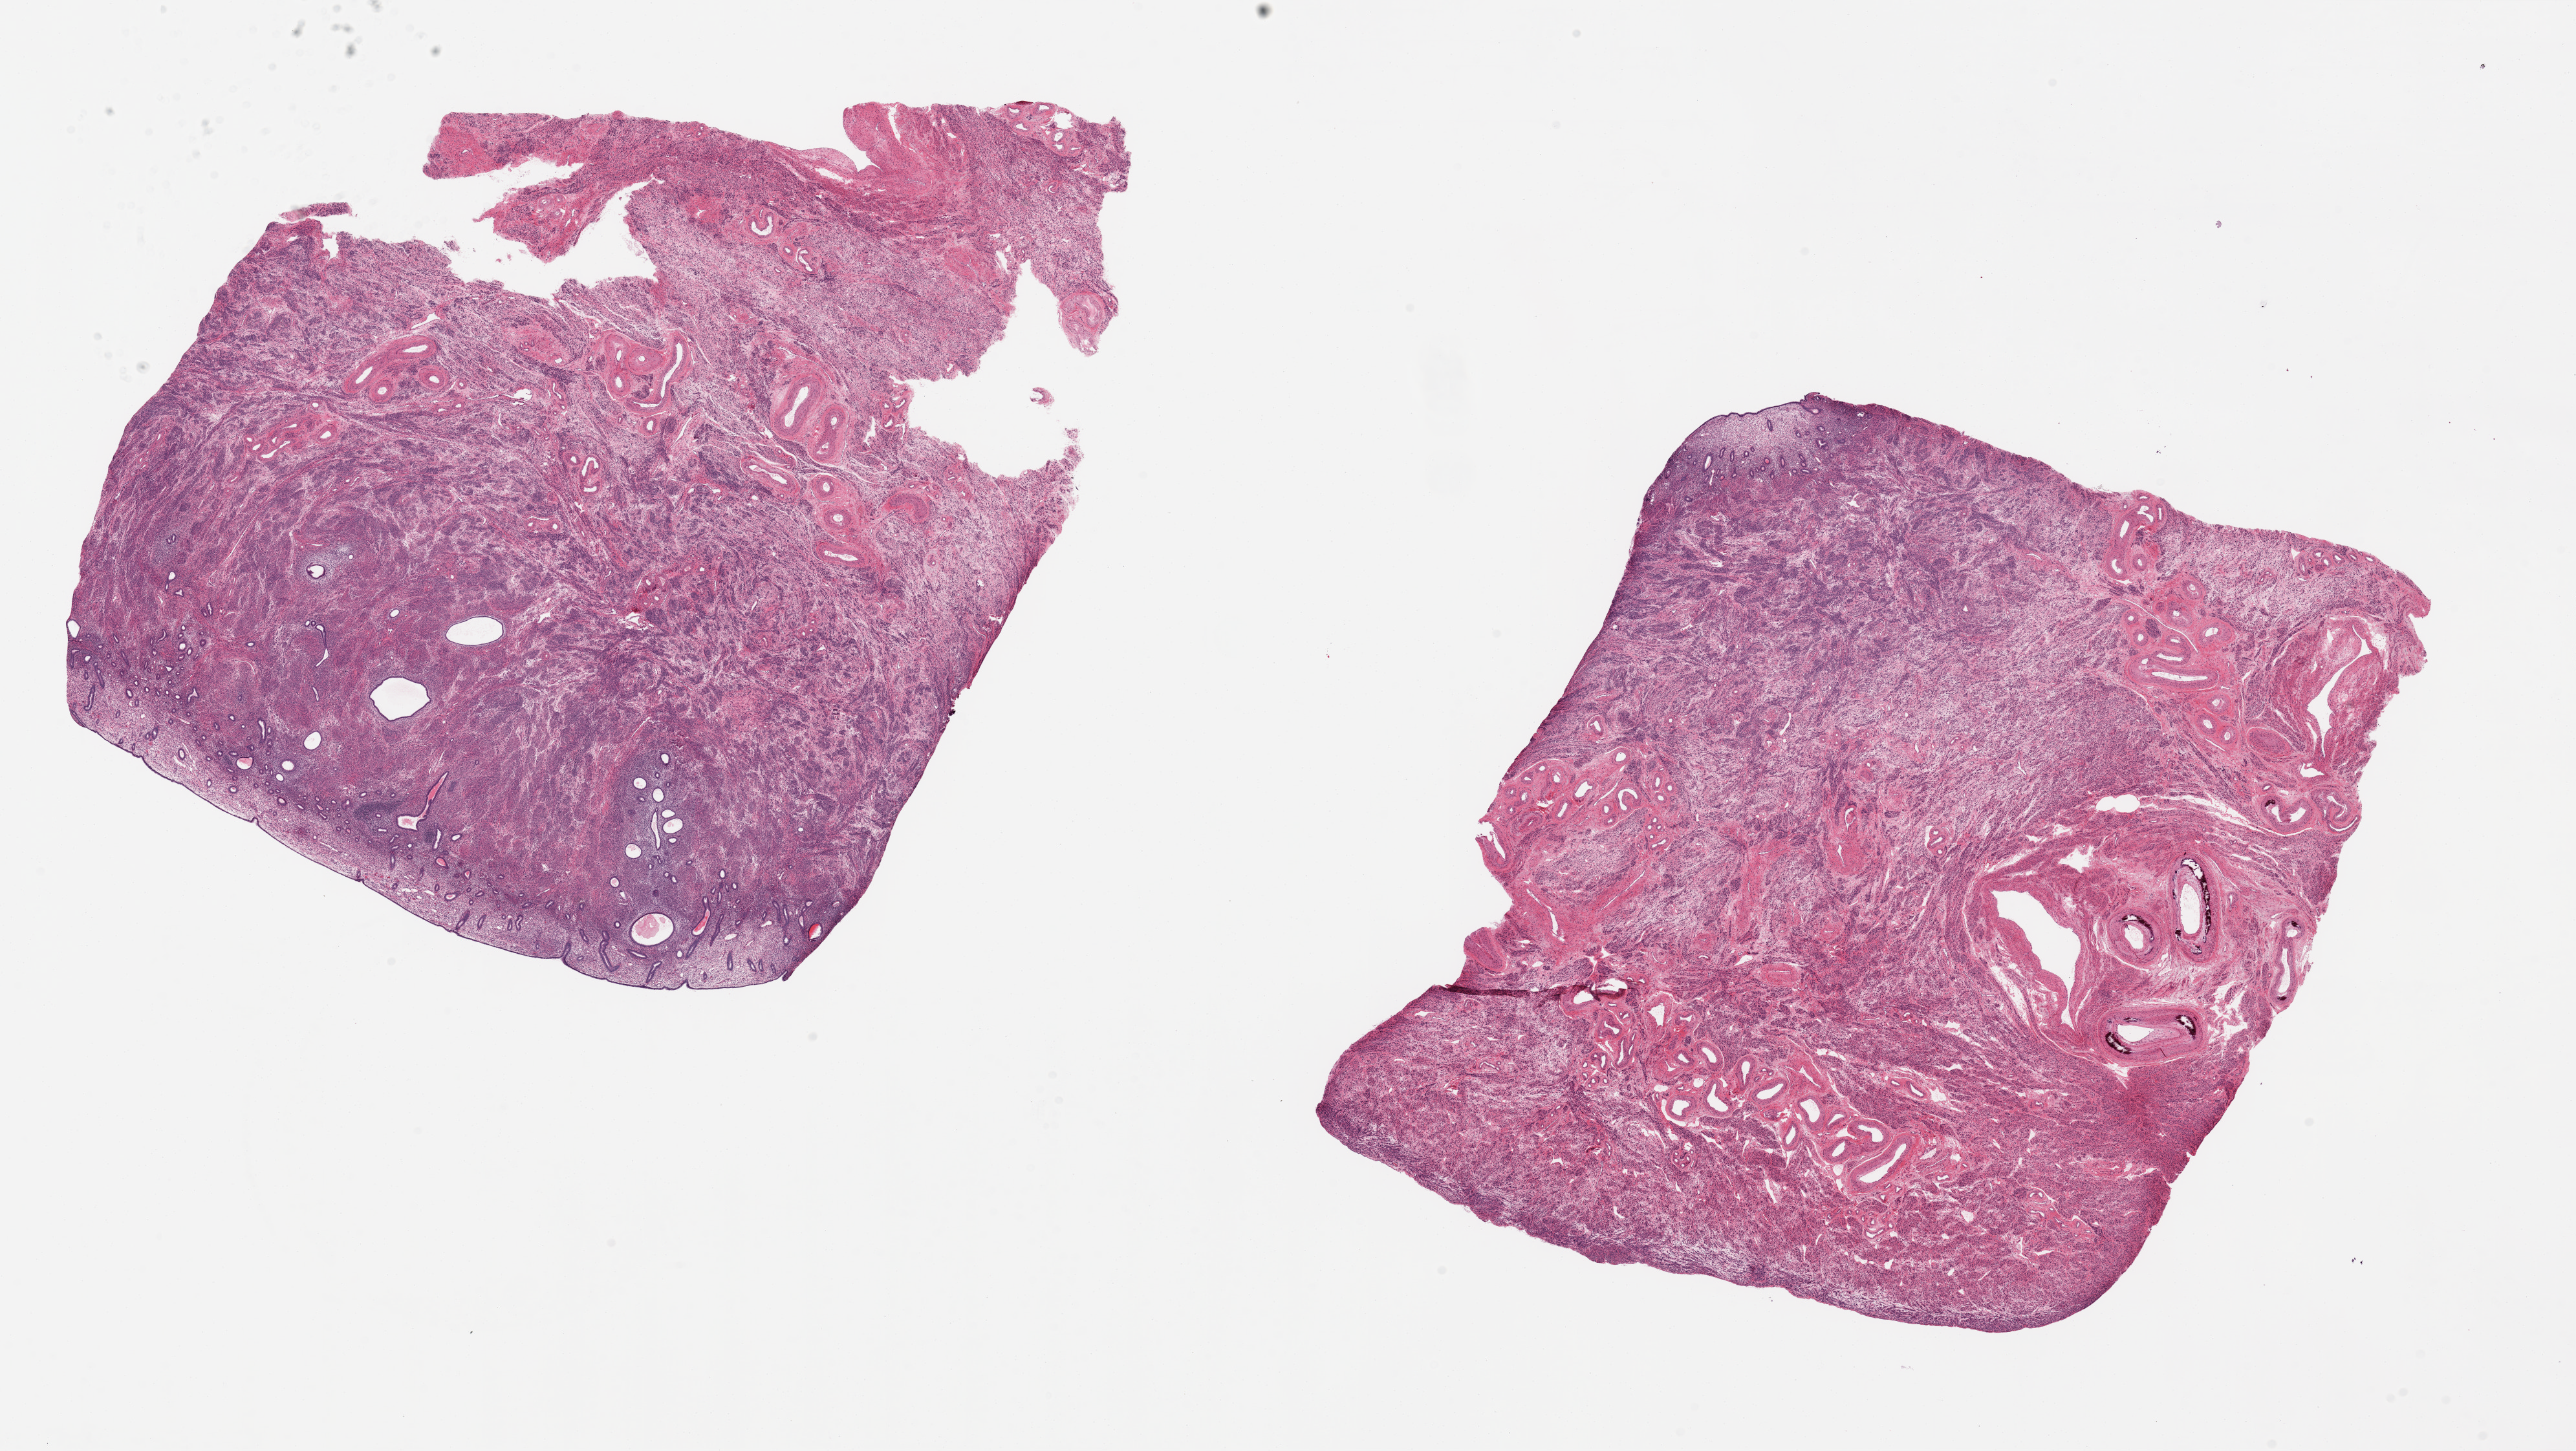
Whole-slide image, H&E stain, low-resolution overview of the scanned area, about 31.5 x 17.7 mm (slide scanned at 20x), PAXgene-fixed paraffin-embedded (PFPE) section, sampled site (target tissue): uterus, donor tissue sample. Donor: female.
Pathologist's review note for this sample: 2 pieces, 13x11 & 11x10mm; up to ~1mm thick atrophic endometrium, foci fo adenomyosis.